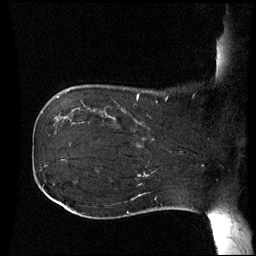
Breast MRI (dynamic contrast-enhanced), one sagittal slice; position 14 of 60 along the scan axis; dynamic contrast-enhanced series, image 2 of 3 at this slice position (ordered by acquisition); 1.5 T; TE 4.2 ms, TR 8.9 ms; 2.5 mm slice thickness; 256 × 256 image matrix, field of view 230 × 230 mm. Female patient, age 42 years. Case-level facts recorded for this patient, not image findings: setting: breast cancer imaged before/during neoadjuvant chemotherapy; receptor status: HER2-positive.
Outlined on this slice (semi-automatically segmented with operator editing):
- analysis volume of interest (the breast-tissue region the enhancement analysis was run in; not a lesion): bounding box [x1, y1, x2, y2] px = [106, 102, 173, 150]
- tumour enhancement mask (voxels above the 70 % enhancement threshold inside the analysis volume of interest): [137, 138, 144, 146]